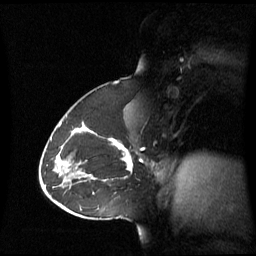
Breast MRI (dynamic contrast-enhanced), one sagittal slice. Position 38 of 60 along the scan axis. Dynamic contrast-enhanced series, image 2 of 3 at this slice position (ordered by acquisition). 1.5 T. TE 4.2 ms, TR 8.4 ms. 2.8 mm slice thickness. 256 × 256 image matrix, field of view 270 × 270 mm. Female patient, age 43 years. Case-level facts recorded for this patient, not image findings: setting: breast cancer imaged before/during neoadjuvant chemotherapy; receptor status: triple-negative.
Annotated regions visible in this slice (semi-automatically segmented with operator editing):
- analysis volume of interest (the breast-tissue region the enhancement analysis was run in; not a lesion): bounding box <62,124,137,180> (left, top, right, bottom; pixels)
- tumour enhancement mask (voxels above the 70 % enhancement threshold inside the analysis volume of interest): <91,131,133,171>